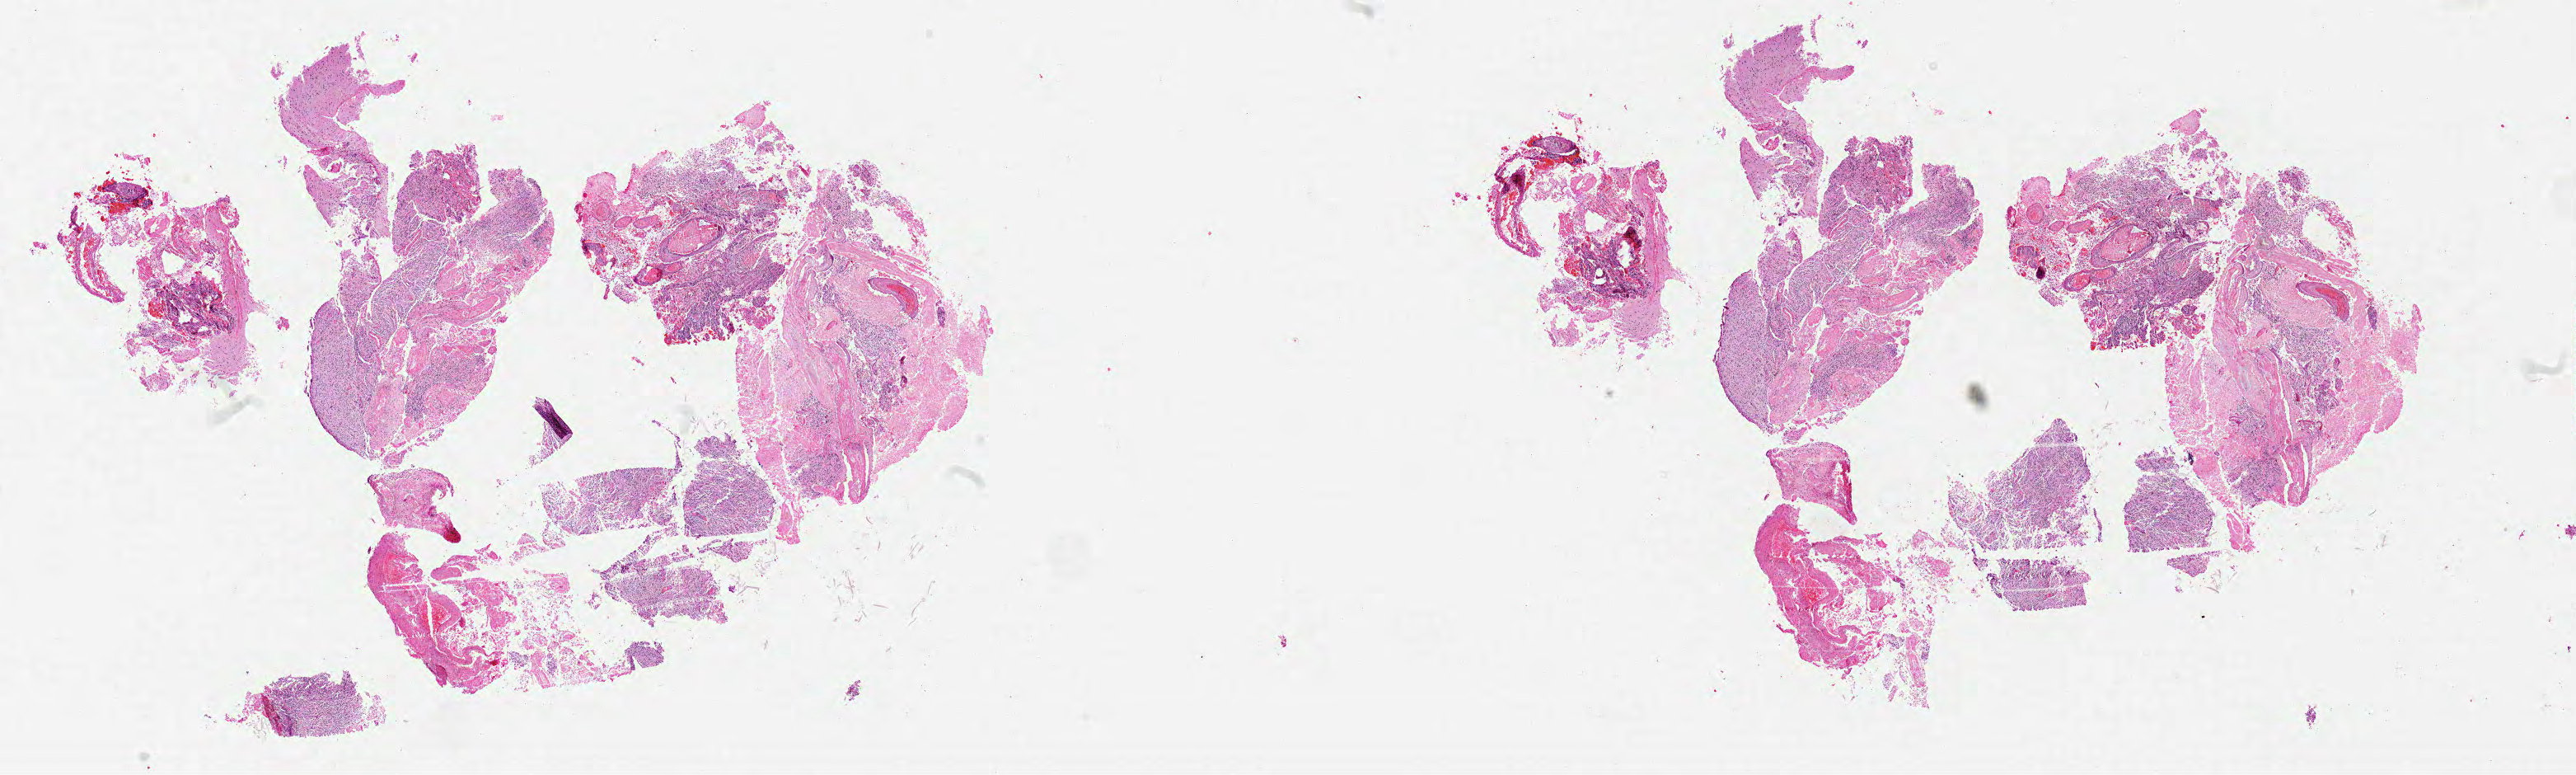
Whole-slide histology image, H&E — shown as a low-resolution overview of the whole scanned area (about 25.0 x 7.5 mm, acquisition: 20x scan); formalin-fixed paraffin-embedded (FFPE) diagnostic section; brain, primary tumour sample. Patient: male, age at initial diagnosis 46 years.
Pathologic diagnosis: Glioblastoma.